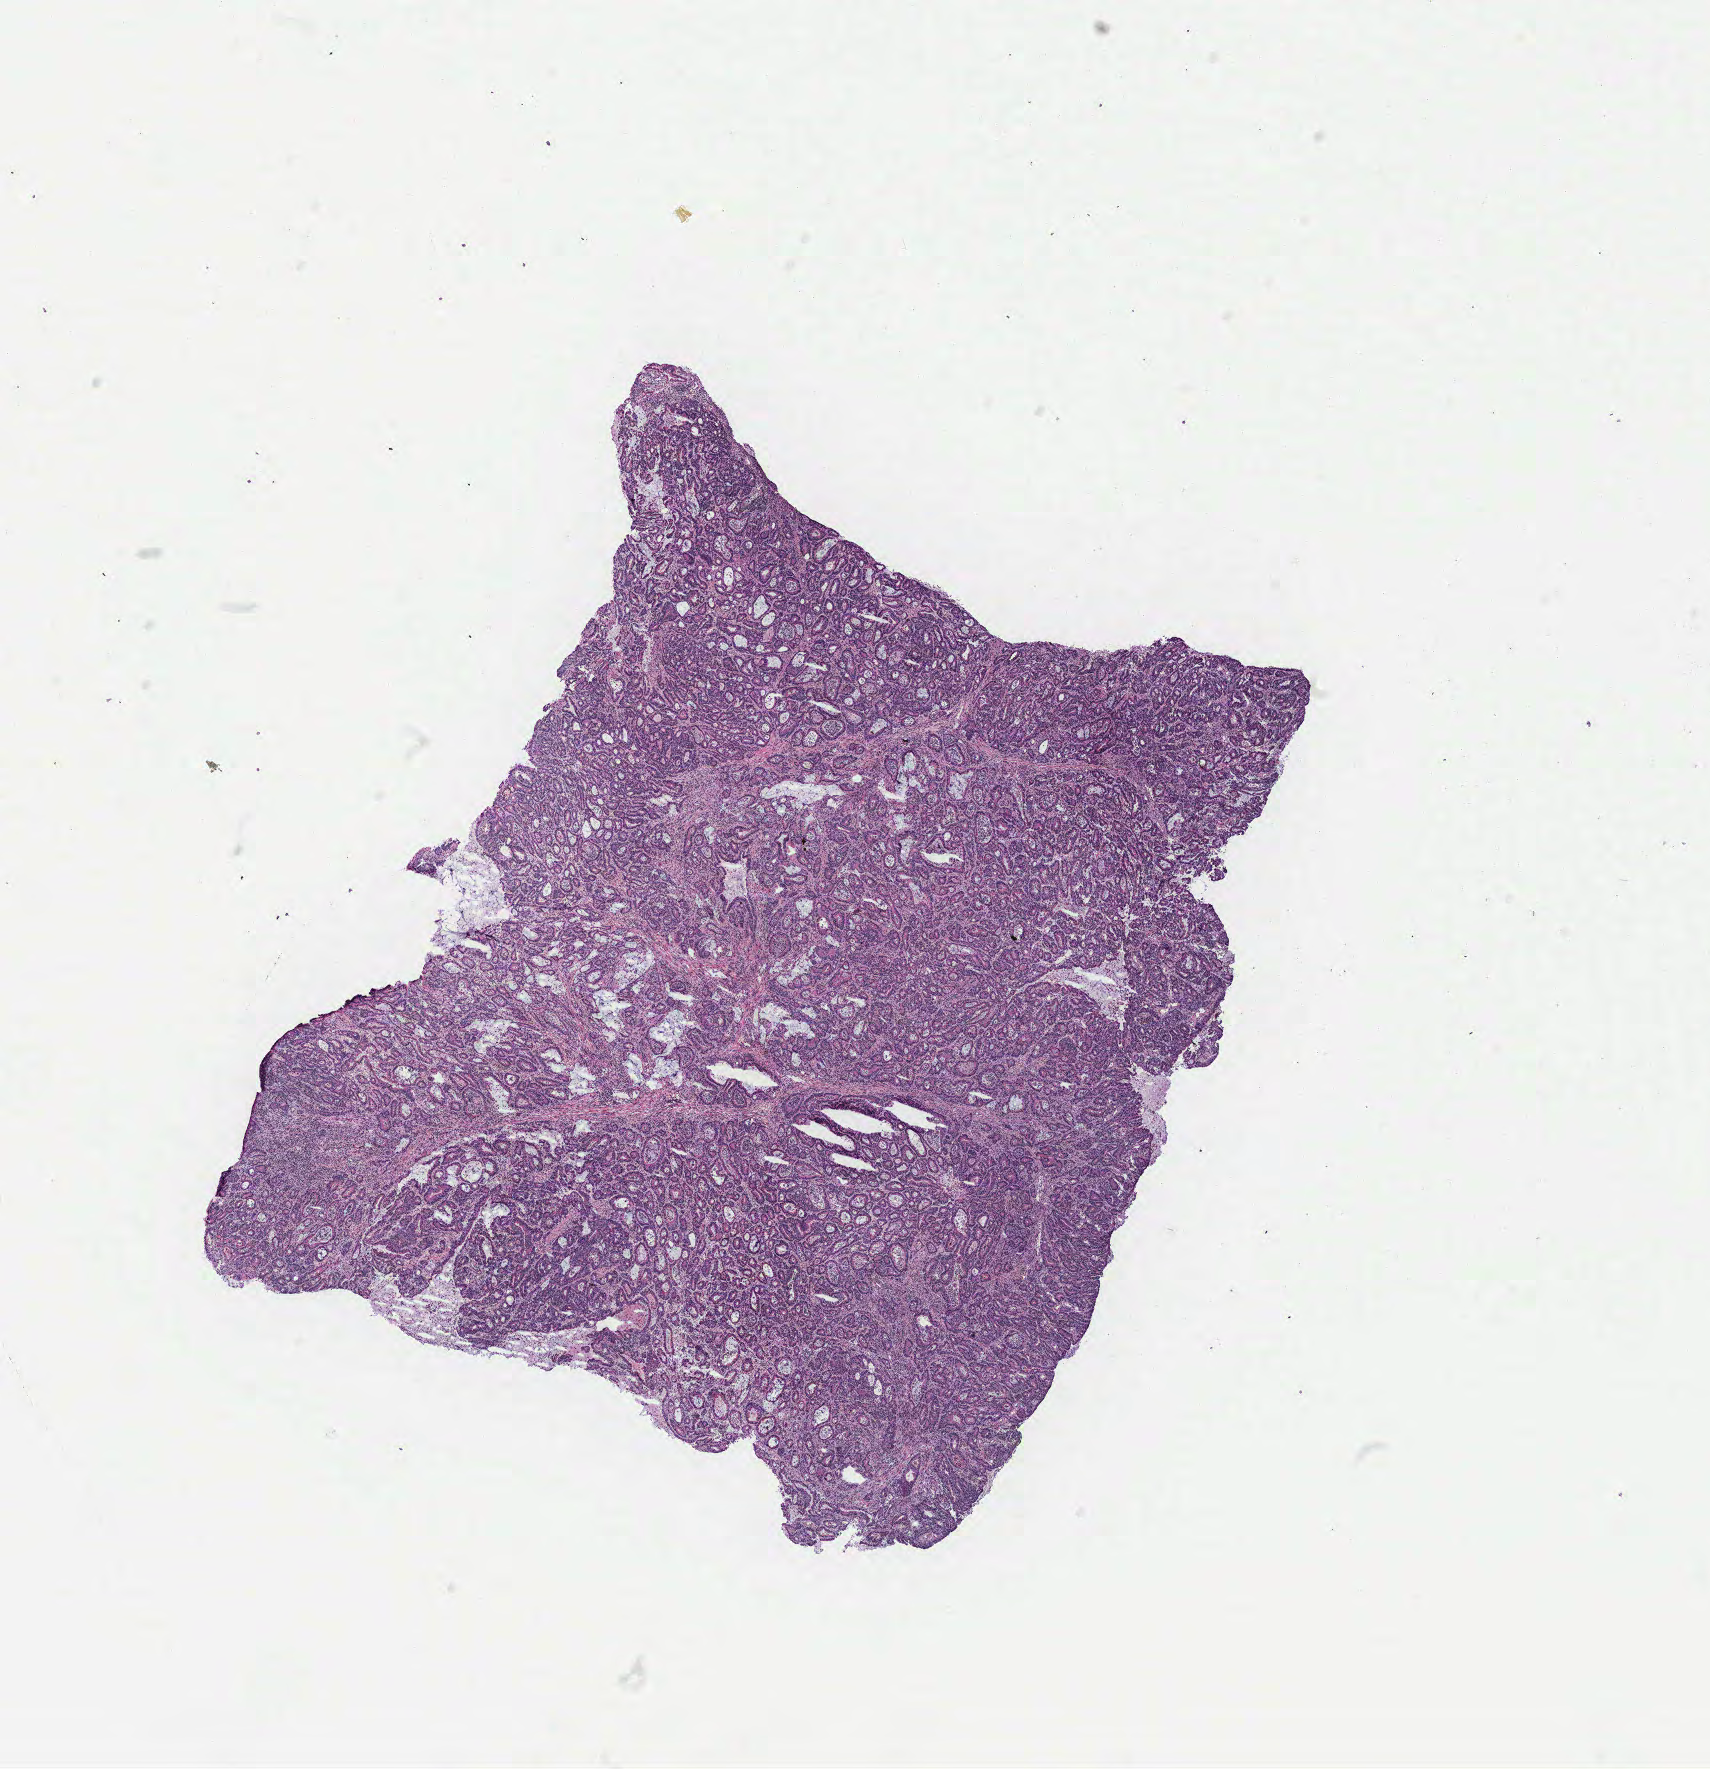
Whole-slide histology image, Hematoxylin and eosin (H&E) stained, low-resolution overview of the scanned area, about 13.7 x 14.2 mm, colon, tumour tissue. 74-year-old female patient.
- diagnosis: Adenocarcinoma, NOS
- AJCC pathologic stage: IIIB
- primary tumour site (as recorded): colon